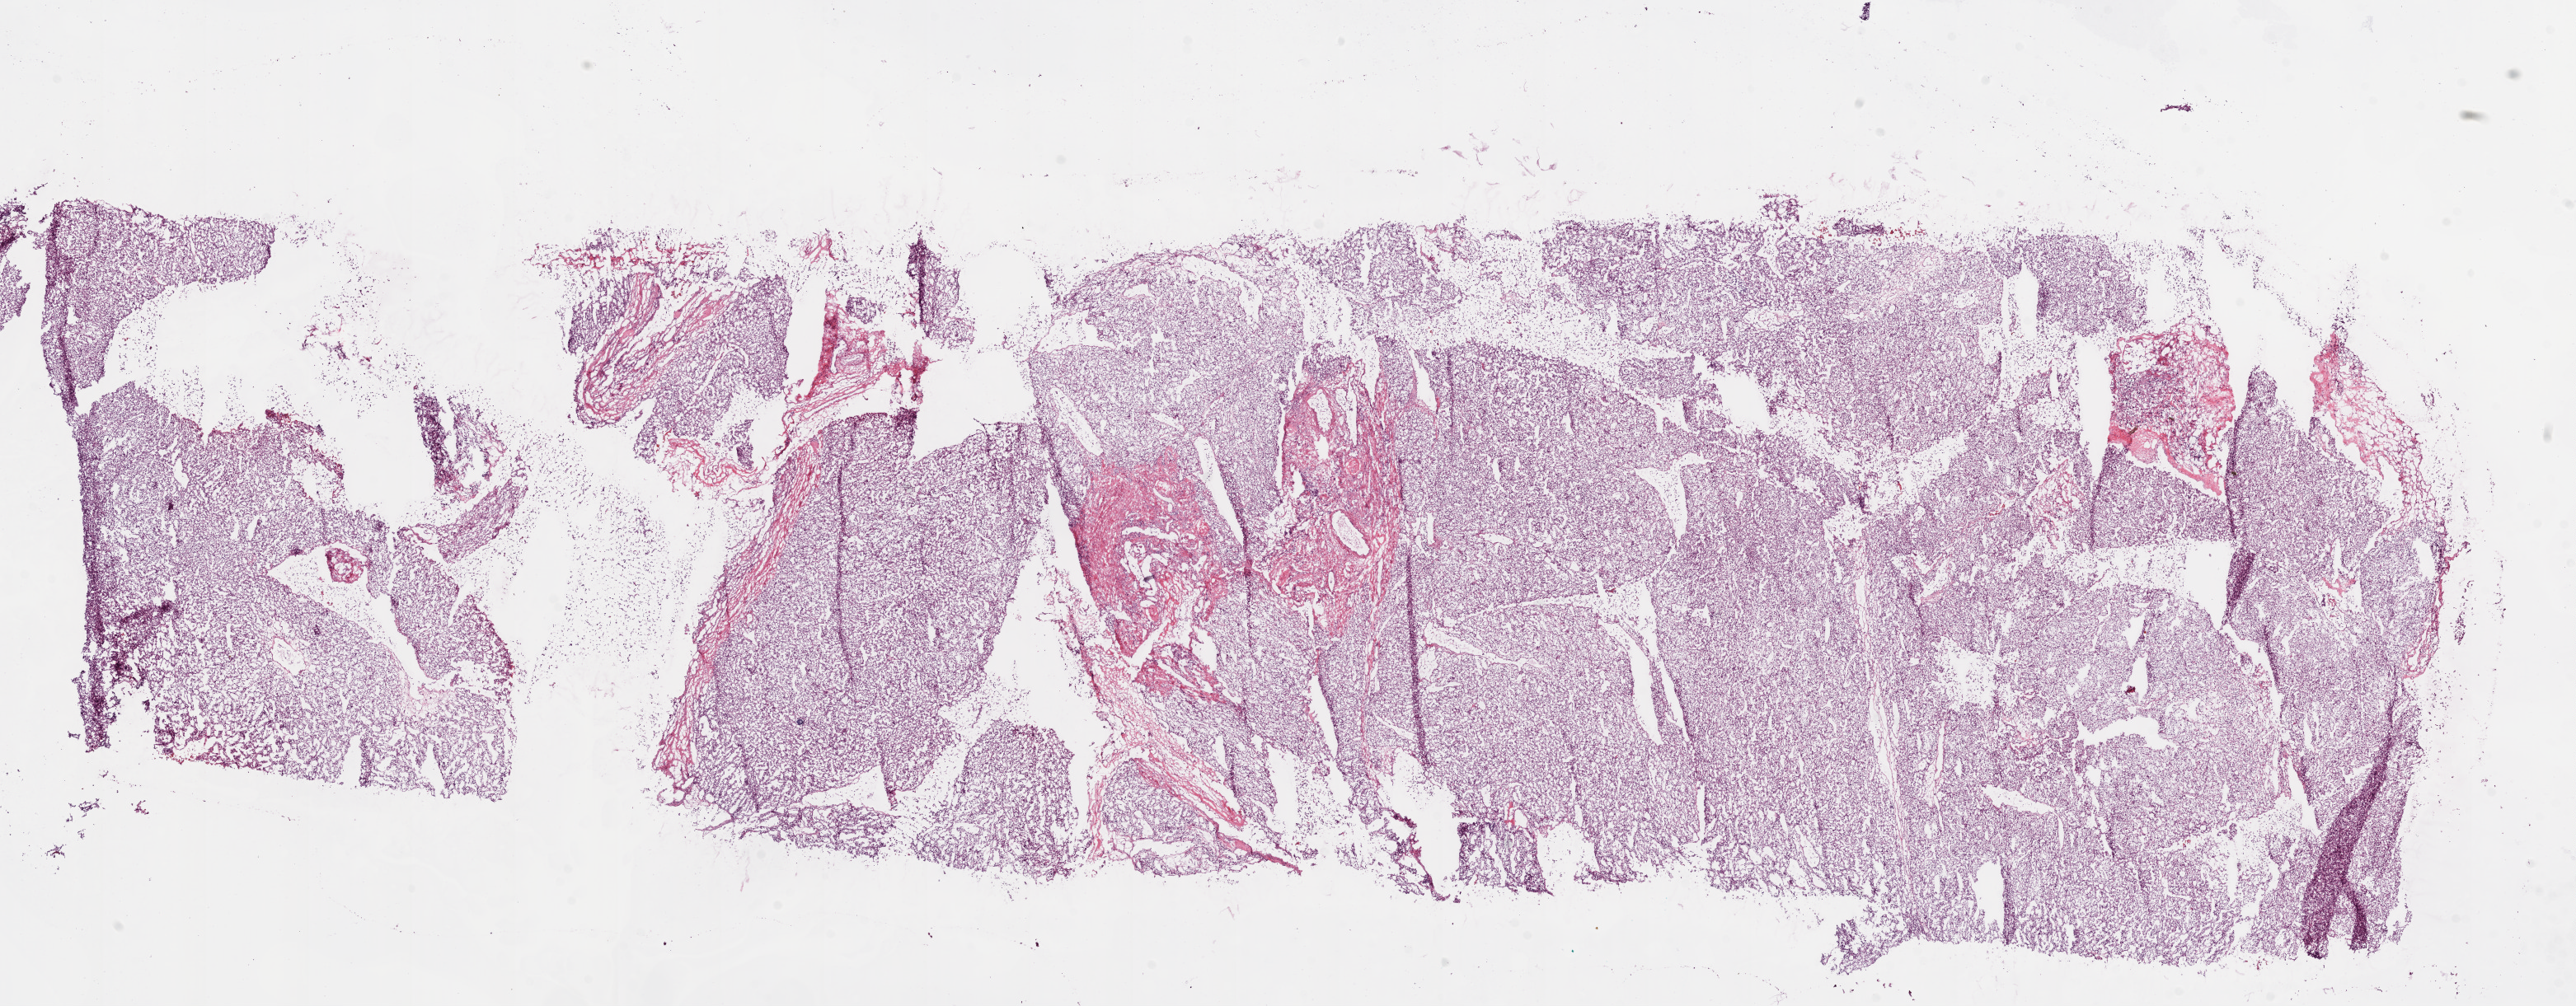
Digitized H&E-stained tissue section (whole slide) — whole scanned area (about 25.1 x 9.8 mm) shown as a low-resolution overview. Frozen section from the bottom of the tissue portion. Kidney, primary tumour sample. Female patient; age at initial diagnosis 65 years. Histologic grade: G2 (moderately differentiated). Pathologist review of this section (percent, as recorded): tumour cells 90%, tumour nuclei 85%, normal cells 0%, stromal cells 10%, necrosis 0%.
* AJCC pathologic stage: I
* lymph nodes positive (case pathology): 0 of 2 examined
* pathologic diagnosis: Clear cell adenocarcinoma, NOS